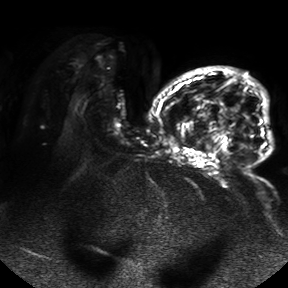
Breast MRI, one axial slice. Position 25 of 50 along the scan axis. Diffusion-weighted series; image 2 of 4 stored at this slice position (different b-values; order by instance number). 1.5 T. 4 mm slice thickness. 288 × 288 image matrix, field of view 390 × 390 mm. Female patient.
Annotated regions visible in this slice (manually delineated by an expert):
- tumour on diffusion-weighted imaging: bounding box [x1, y1, x2, y2] px = [232, 104, 246, 132]